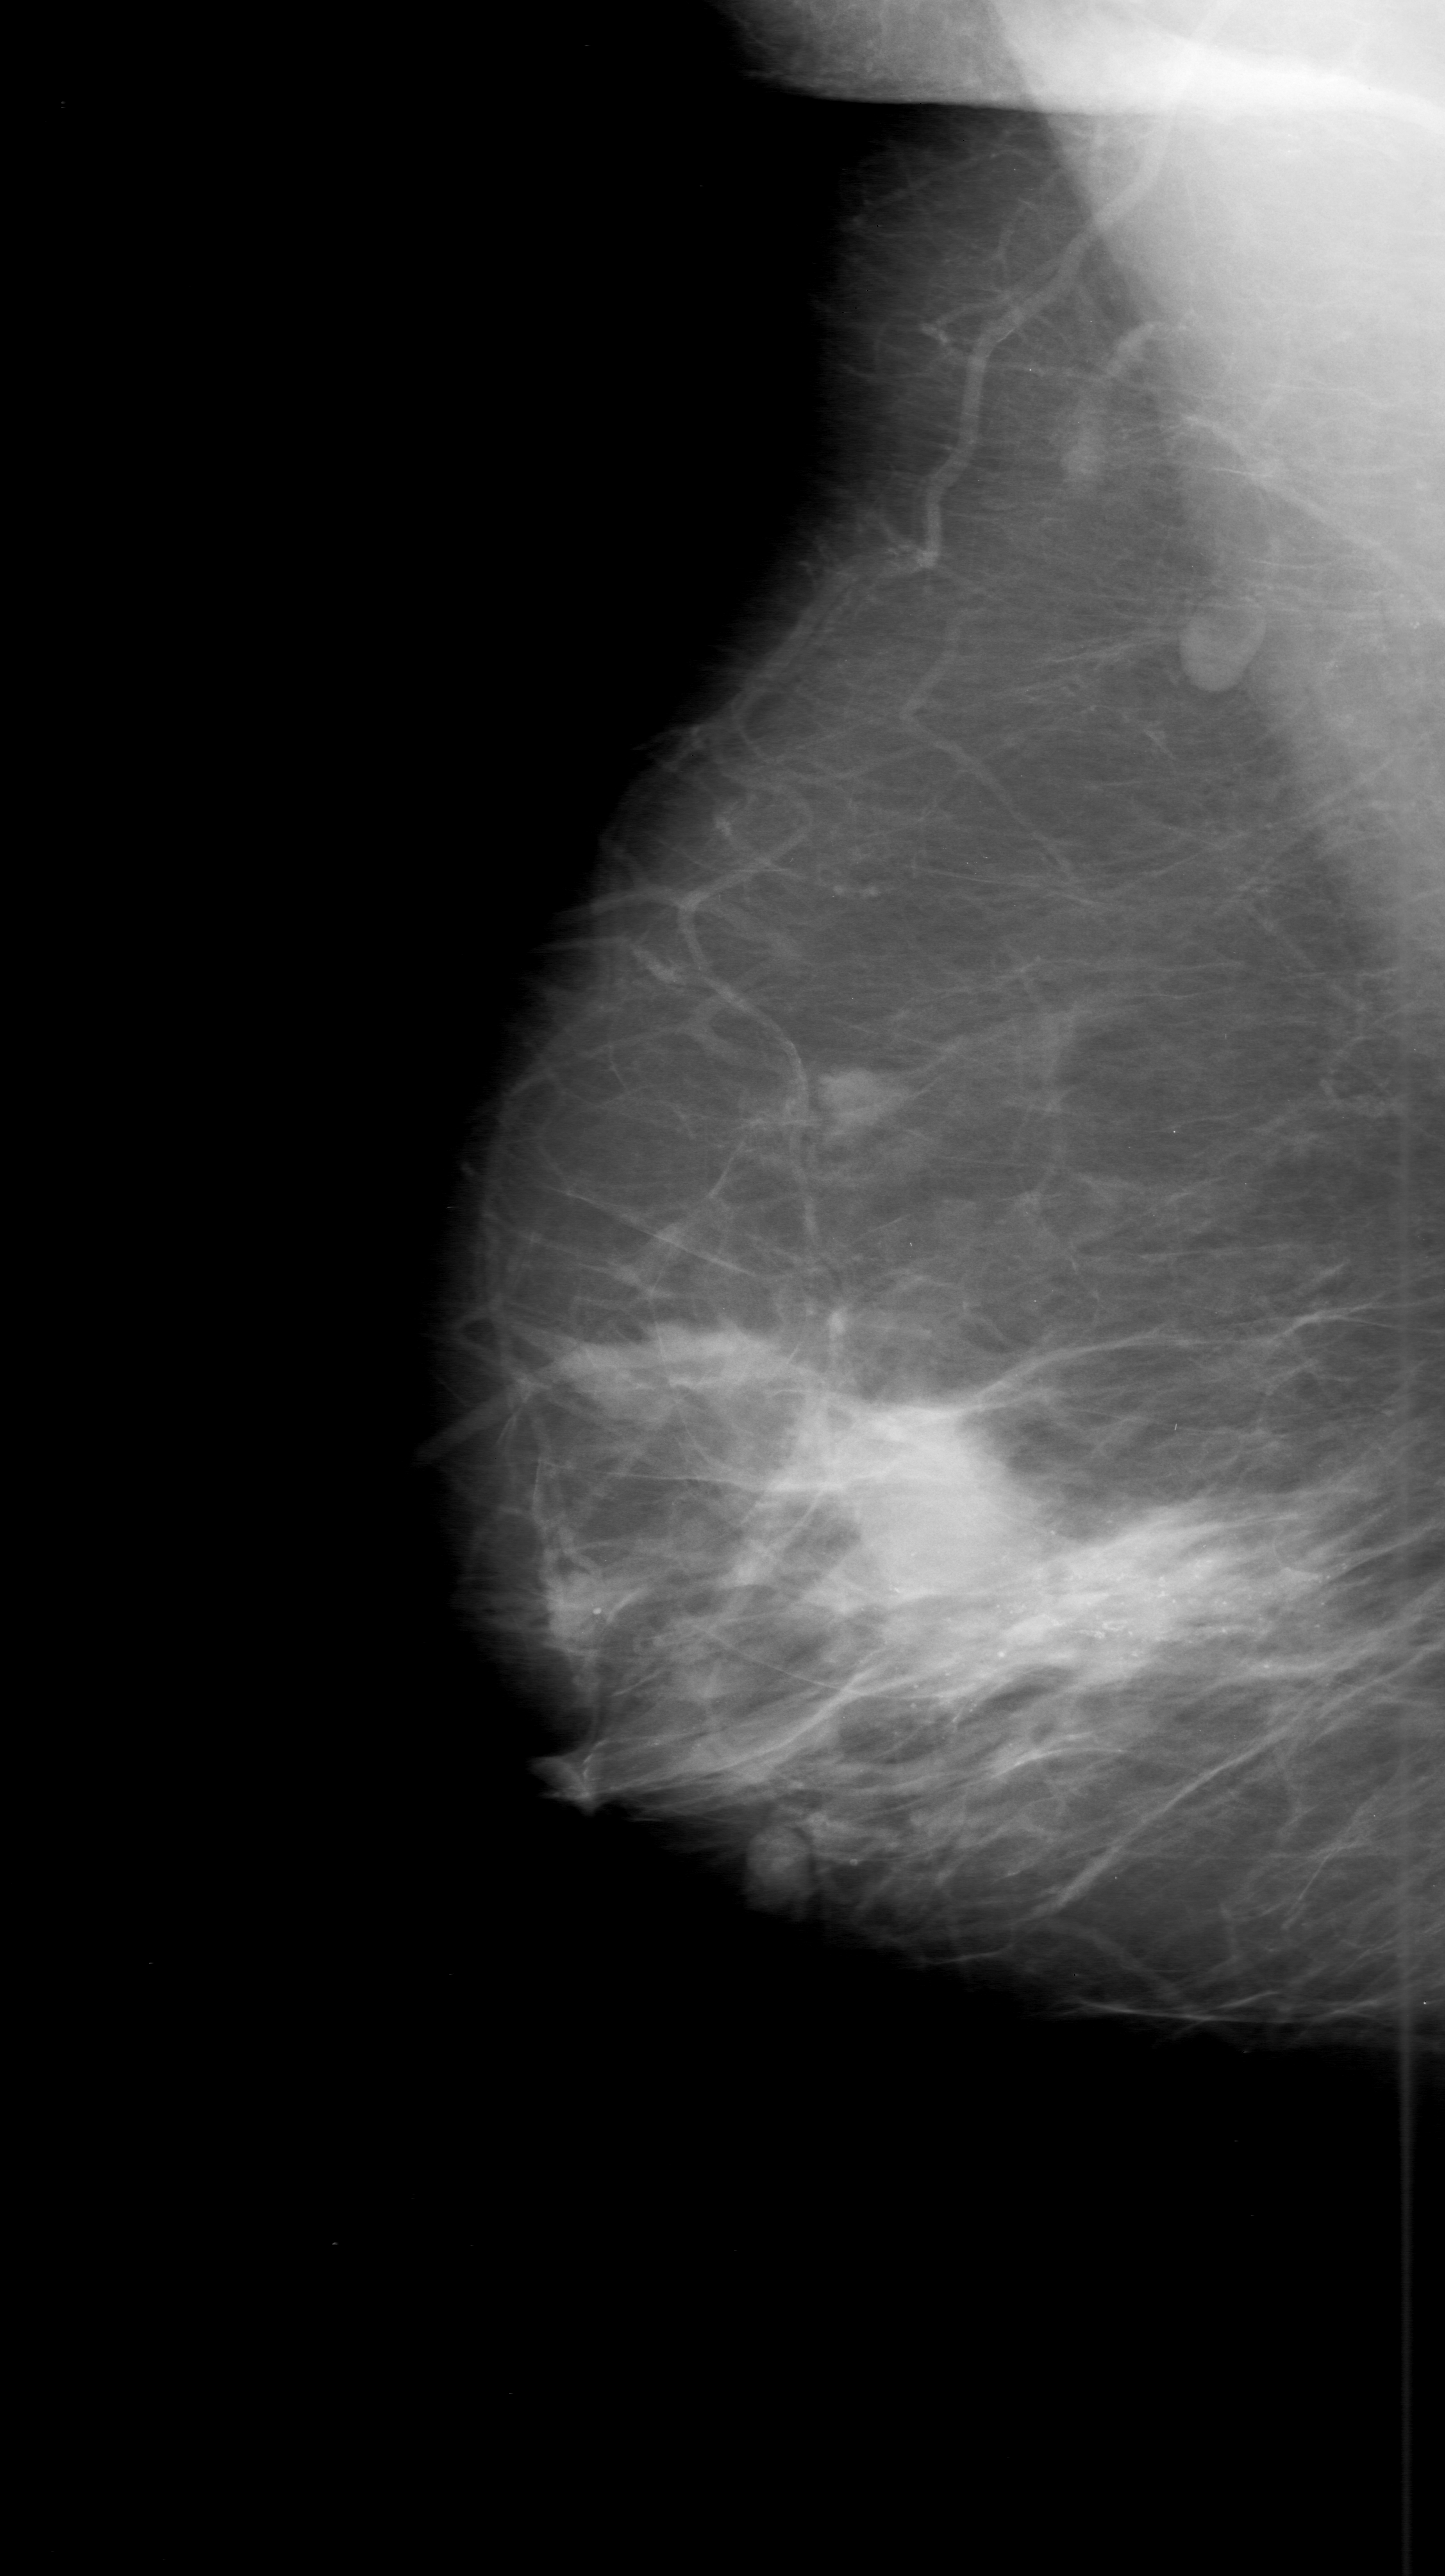
Scanned film-screen mammogram; right breast; mediolateral oblique (MLO) view.
- Marked abnormality: calcifications, morphology amorphous / pleomorphic, distribution segmental; BI-RADS assessment category 5; subtlety rating 5 on a 1 (subtle) to 5 (obvious) scale; pathology (as recorded): malignant.